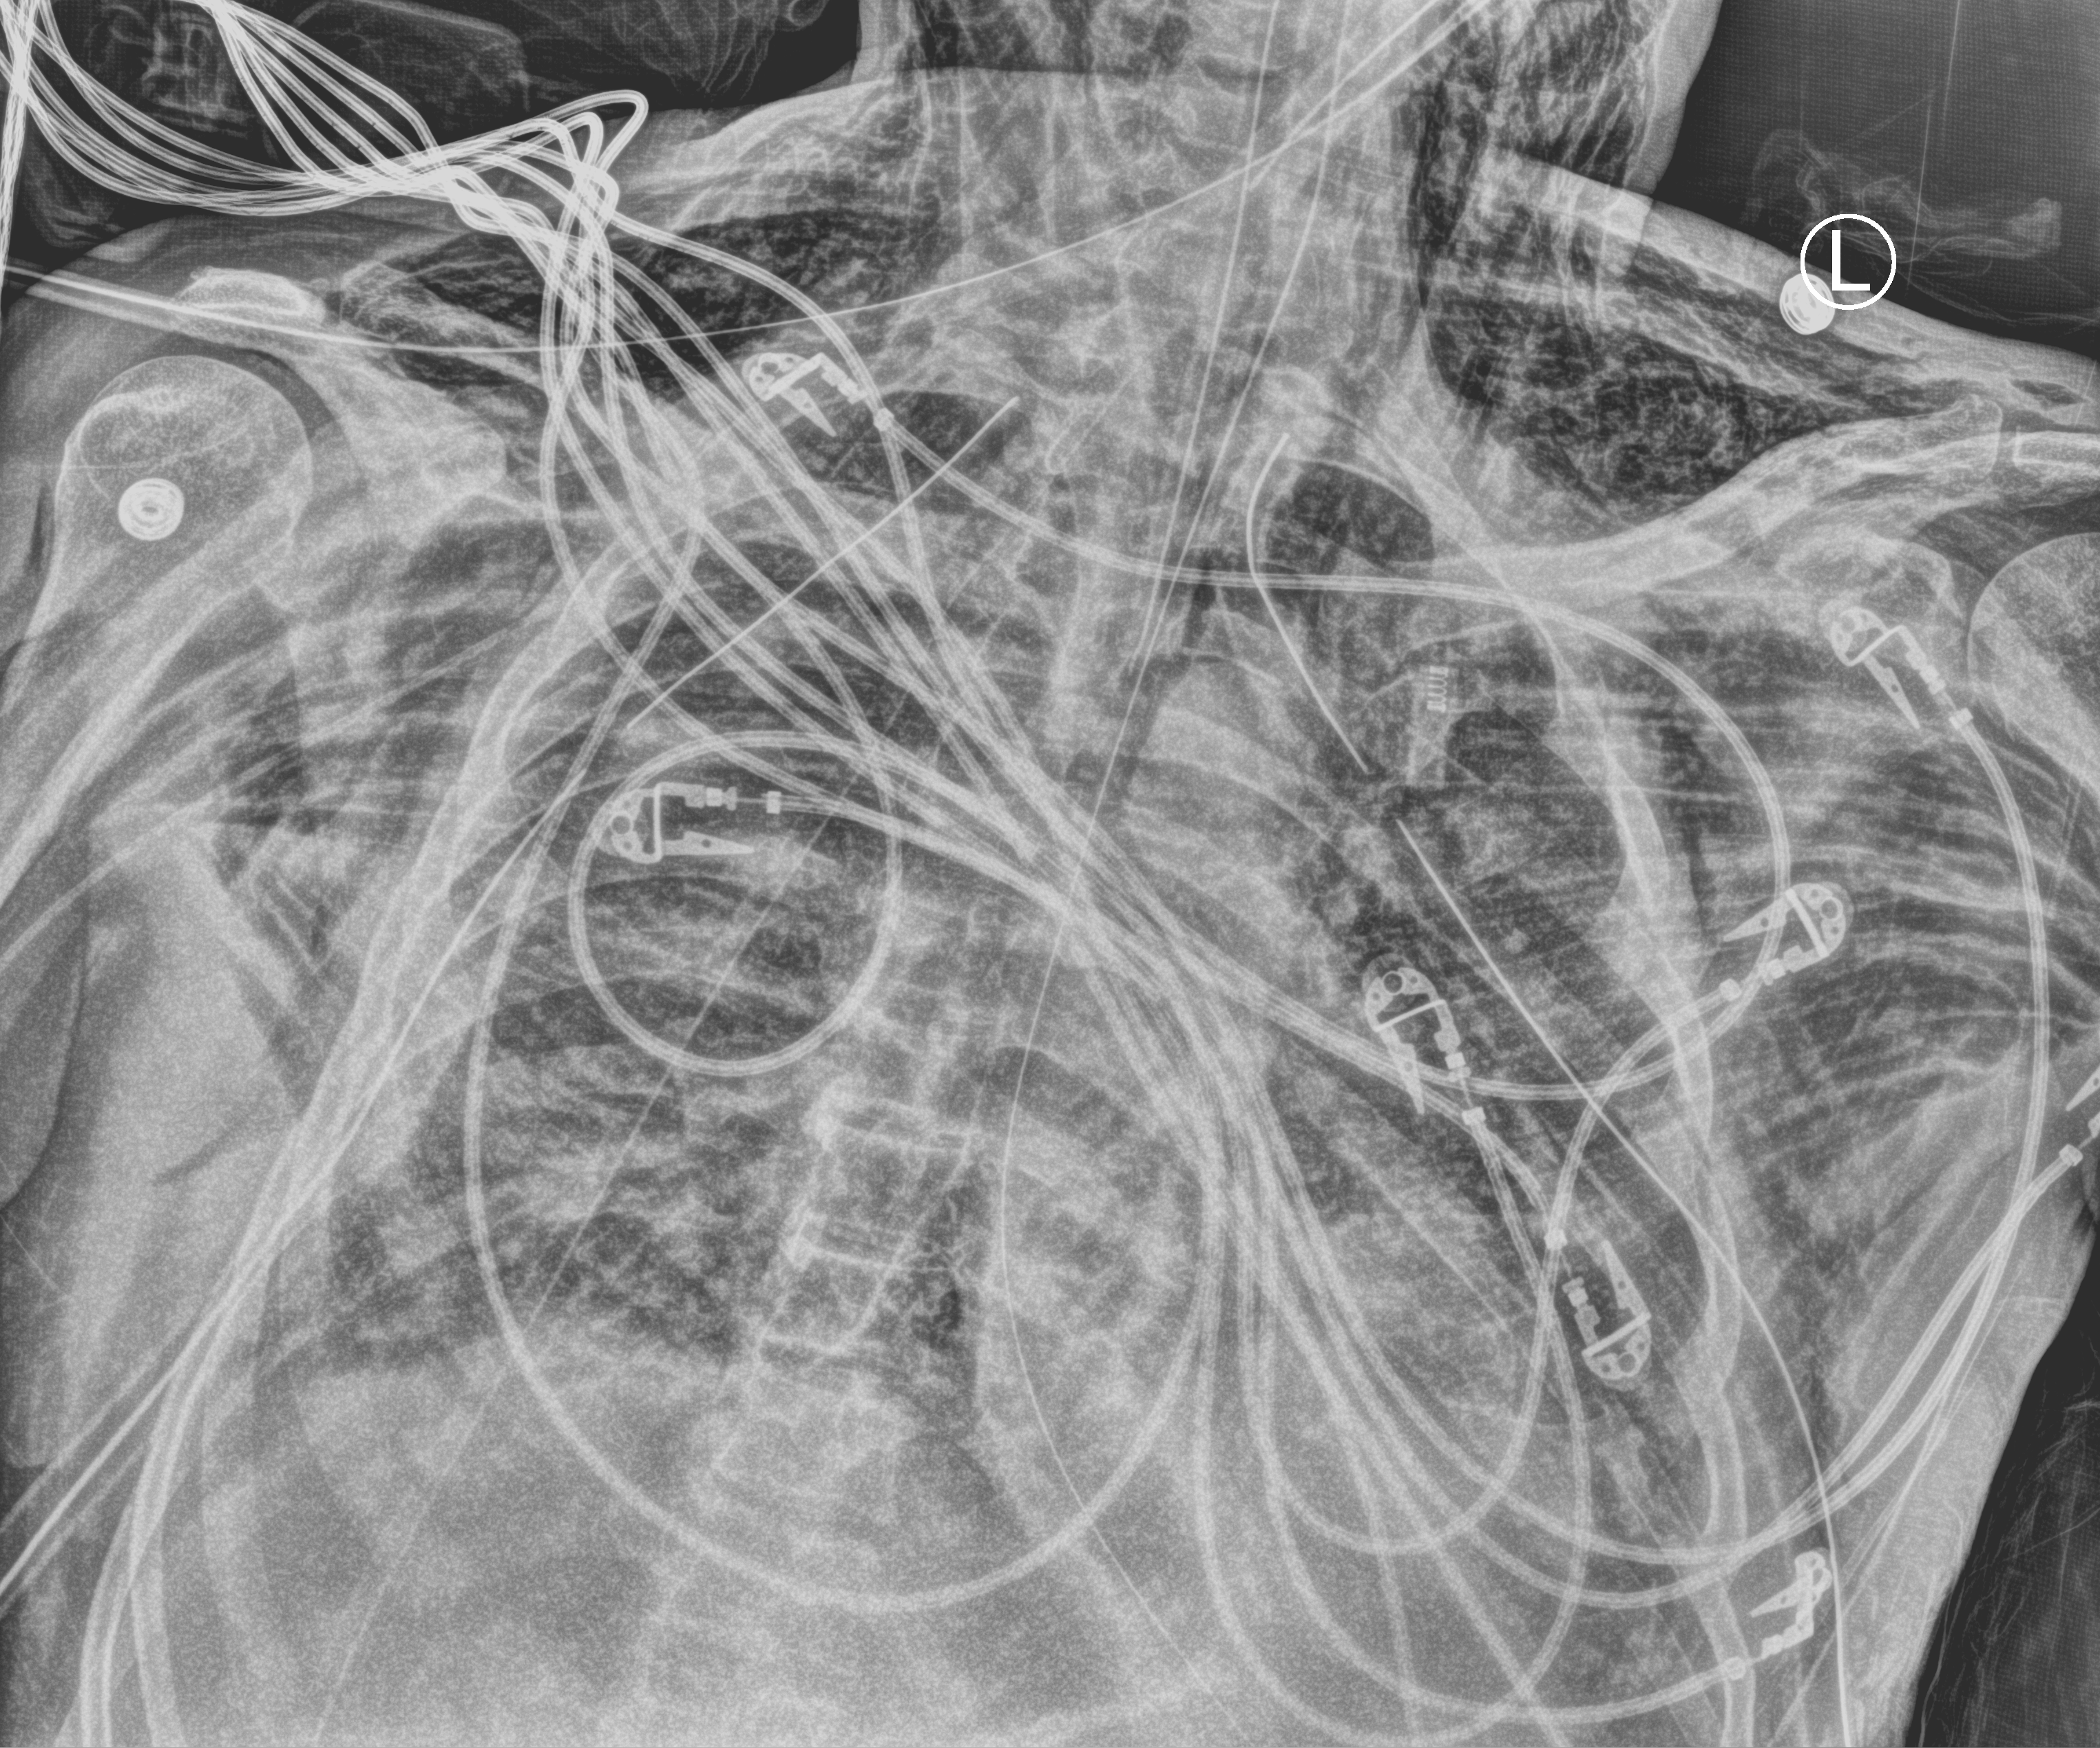
Portable chest radiograph, anteroposterior (AP) projection. Male patient hospitalised with COVID-19, age 18–59 years.
Admission-level facts for this patient (not findings on this image; timing relative to this image not recorded): admitted to intensive care during this hospital stay: yes; mechanically ventilated during this hospital stay: yes.